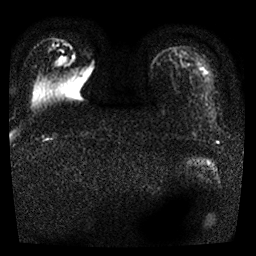
Breast MRI, one axial slice; position 3 of 25 along the scan axis; diffusion-weighted series; image 2 of 4 stored at this slice position (different b-values; order by instance number); 1.5 T; 4 mm slice thickness; 256 × 256 image matrix, field of view 290 × 290 mm. Female patient.
Structures marked on this image (outlined manually by an expert reader):
- tumour on diffusion-weighted imaging: bounding box (x1, y1, x2, y2) in pixels: (55, 57, 72, 66)